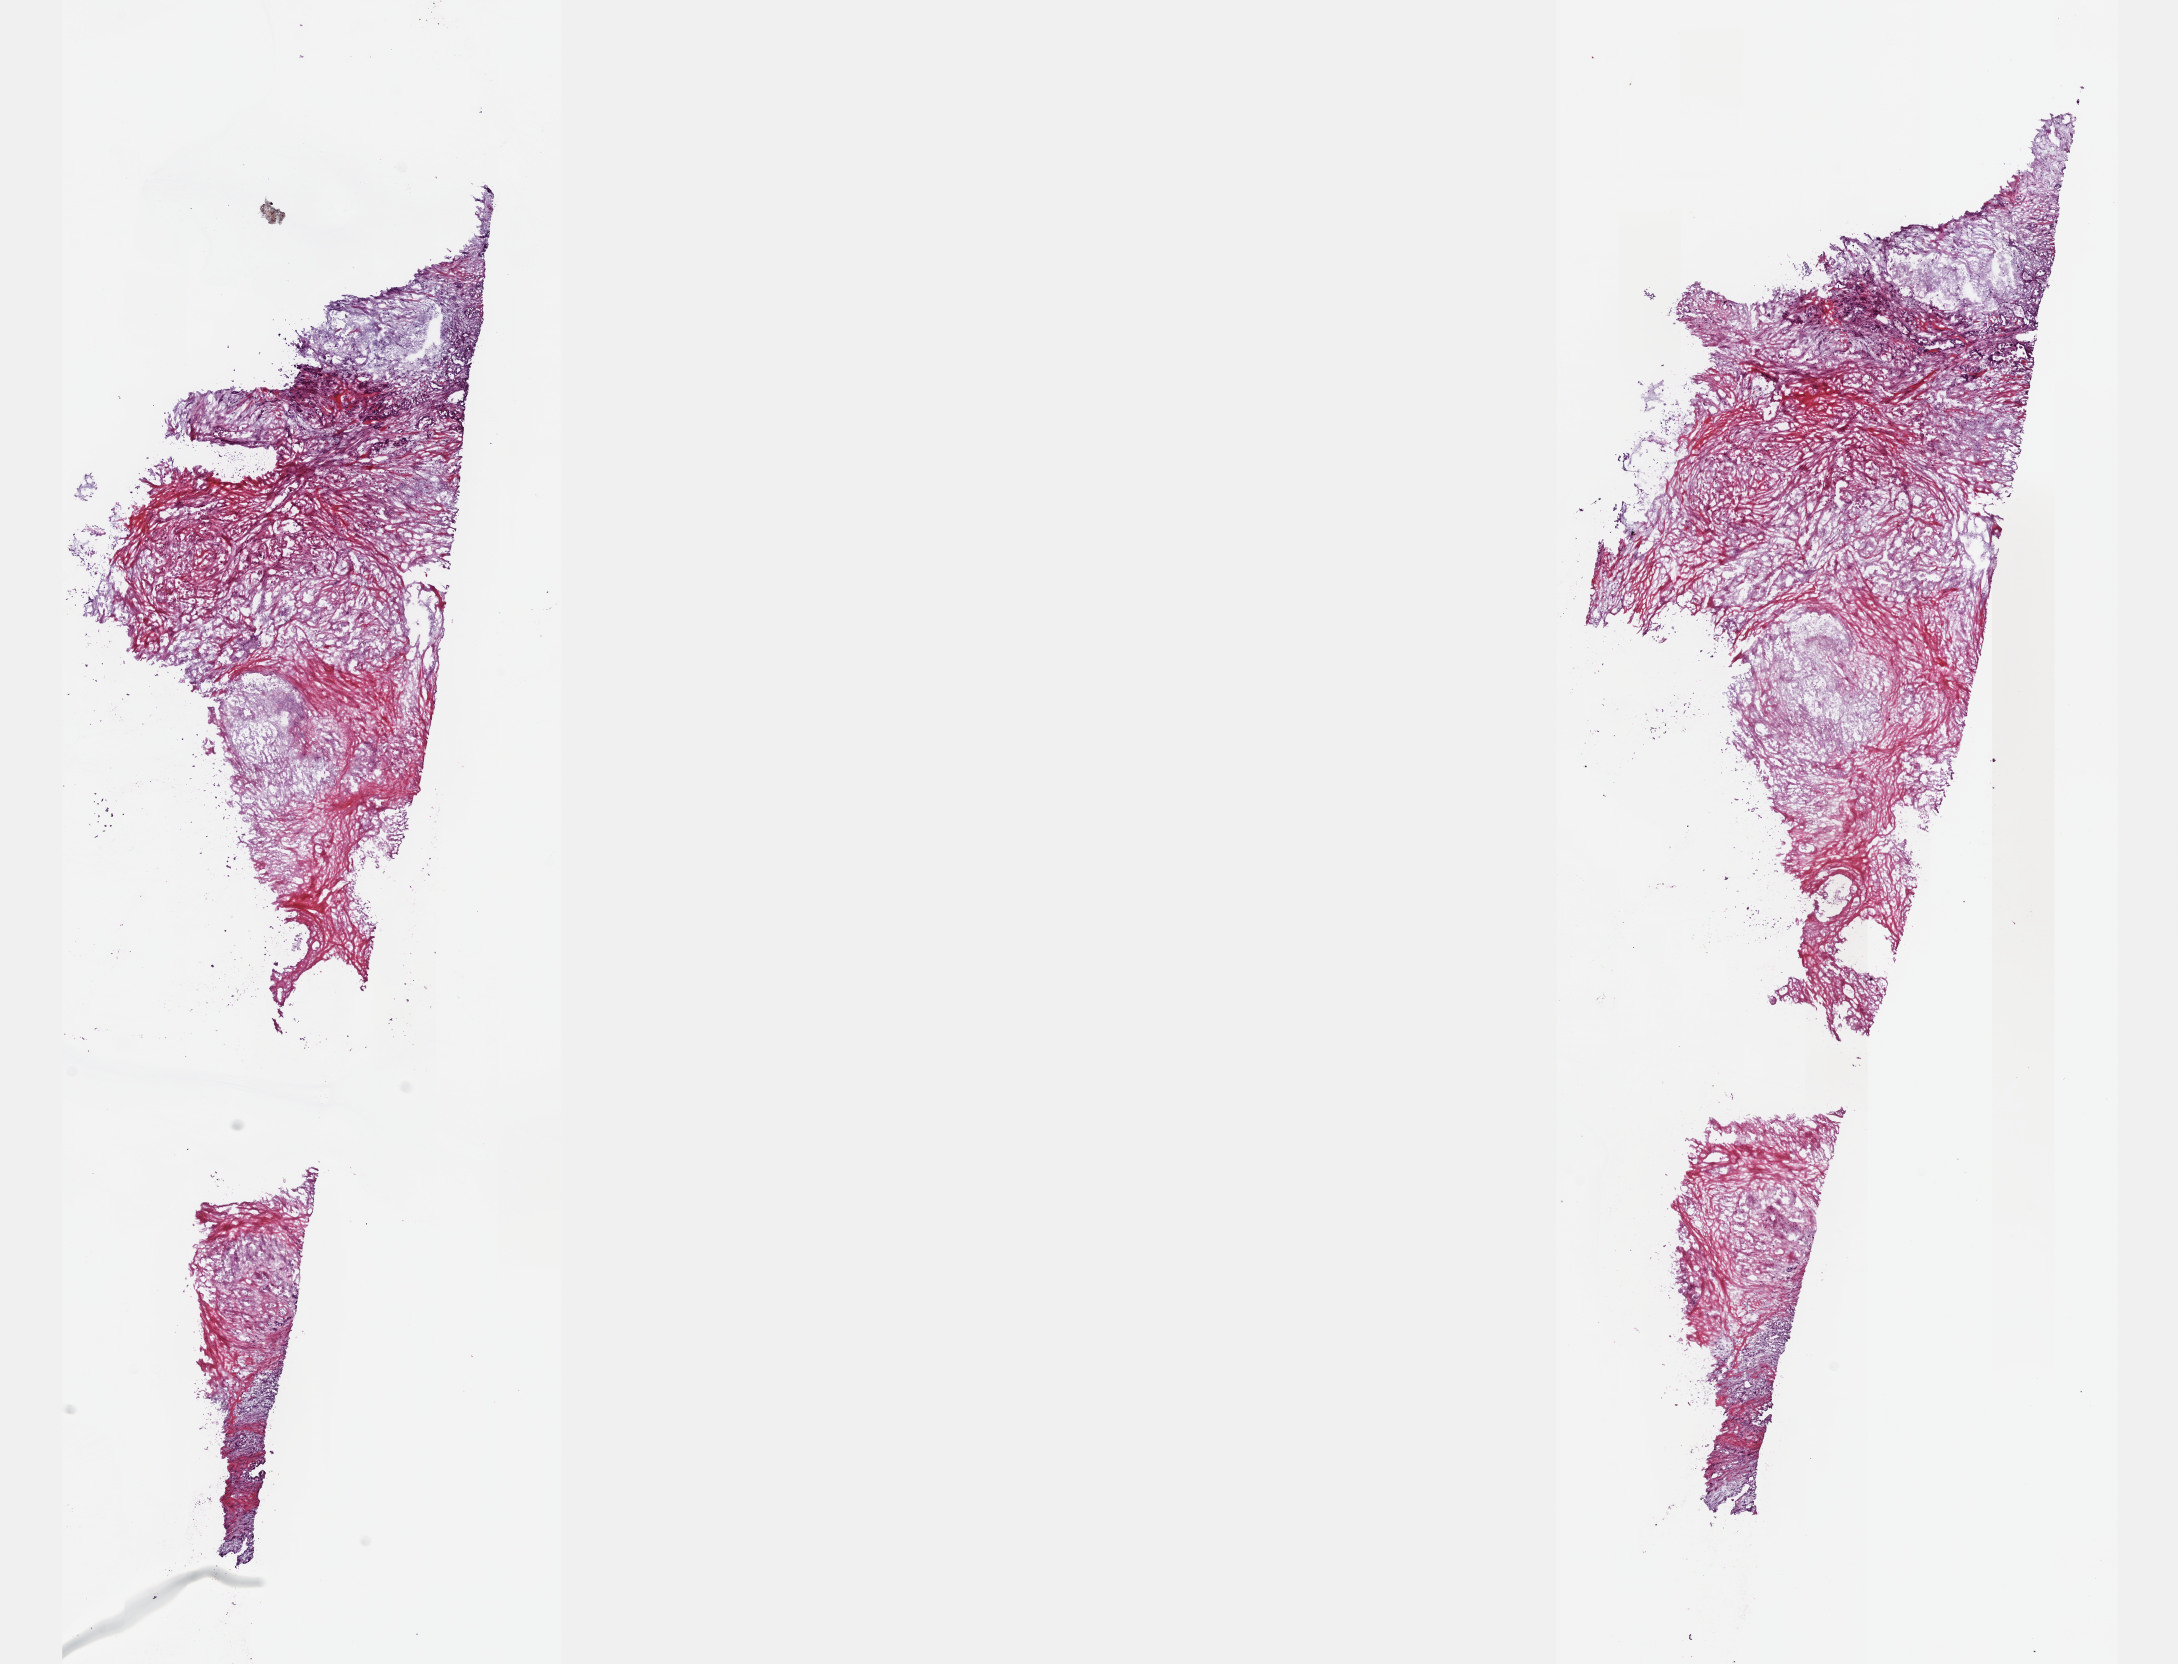
Digitized Hematoxylin and eosin (H&E) stained tissue section (whole slide) — low-resolution overview of the scanned area, about 17.6 x 13.4 mm (slide scanned at 40x). Frozen section from the top of the tissue portion. Sample: primary tumour, pancreas. Patient: male, age at initial diagnosis 50 years. Histologic grade: G2 (moderately differentiated). Composition of this section per pathologist review: tumour cells 40%, tumour nuclei 40%, normal cells 0%, stromal cells 40%, necrosis 20%. Inflammatory infiltration, as recorded: lymphocyte infiltration 40%, monocyte infiltration 20%, neutrophil infiltration 20%.
Histologic diagnosis: Infiltrating duct carcinoma, NOS (tail of pancreas). TNM: T3 N1 M0. AJCC pathologic stage: IIB. Lymph nodes positive (case pathology): 13 of 21 examined.